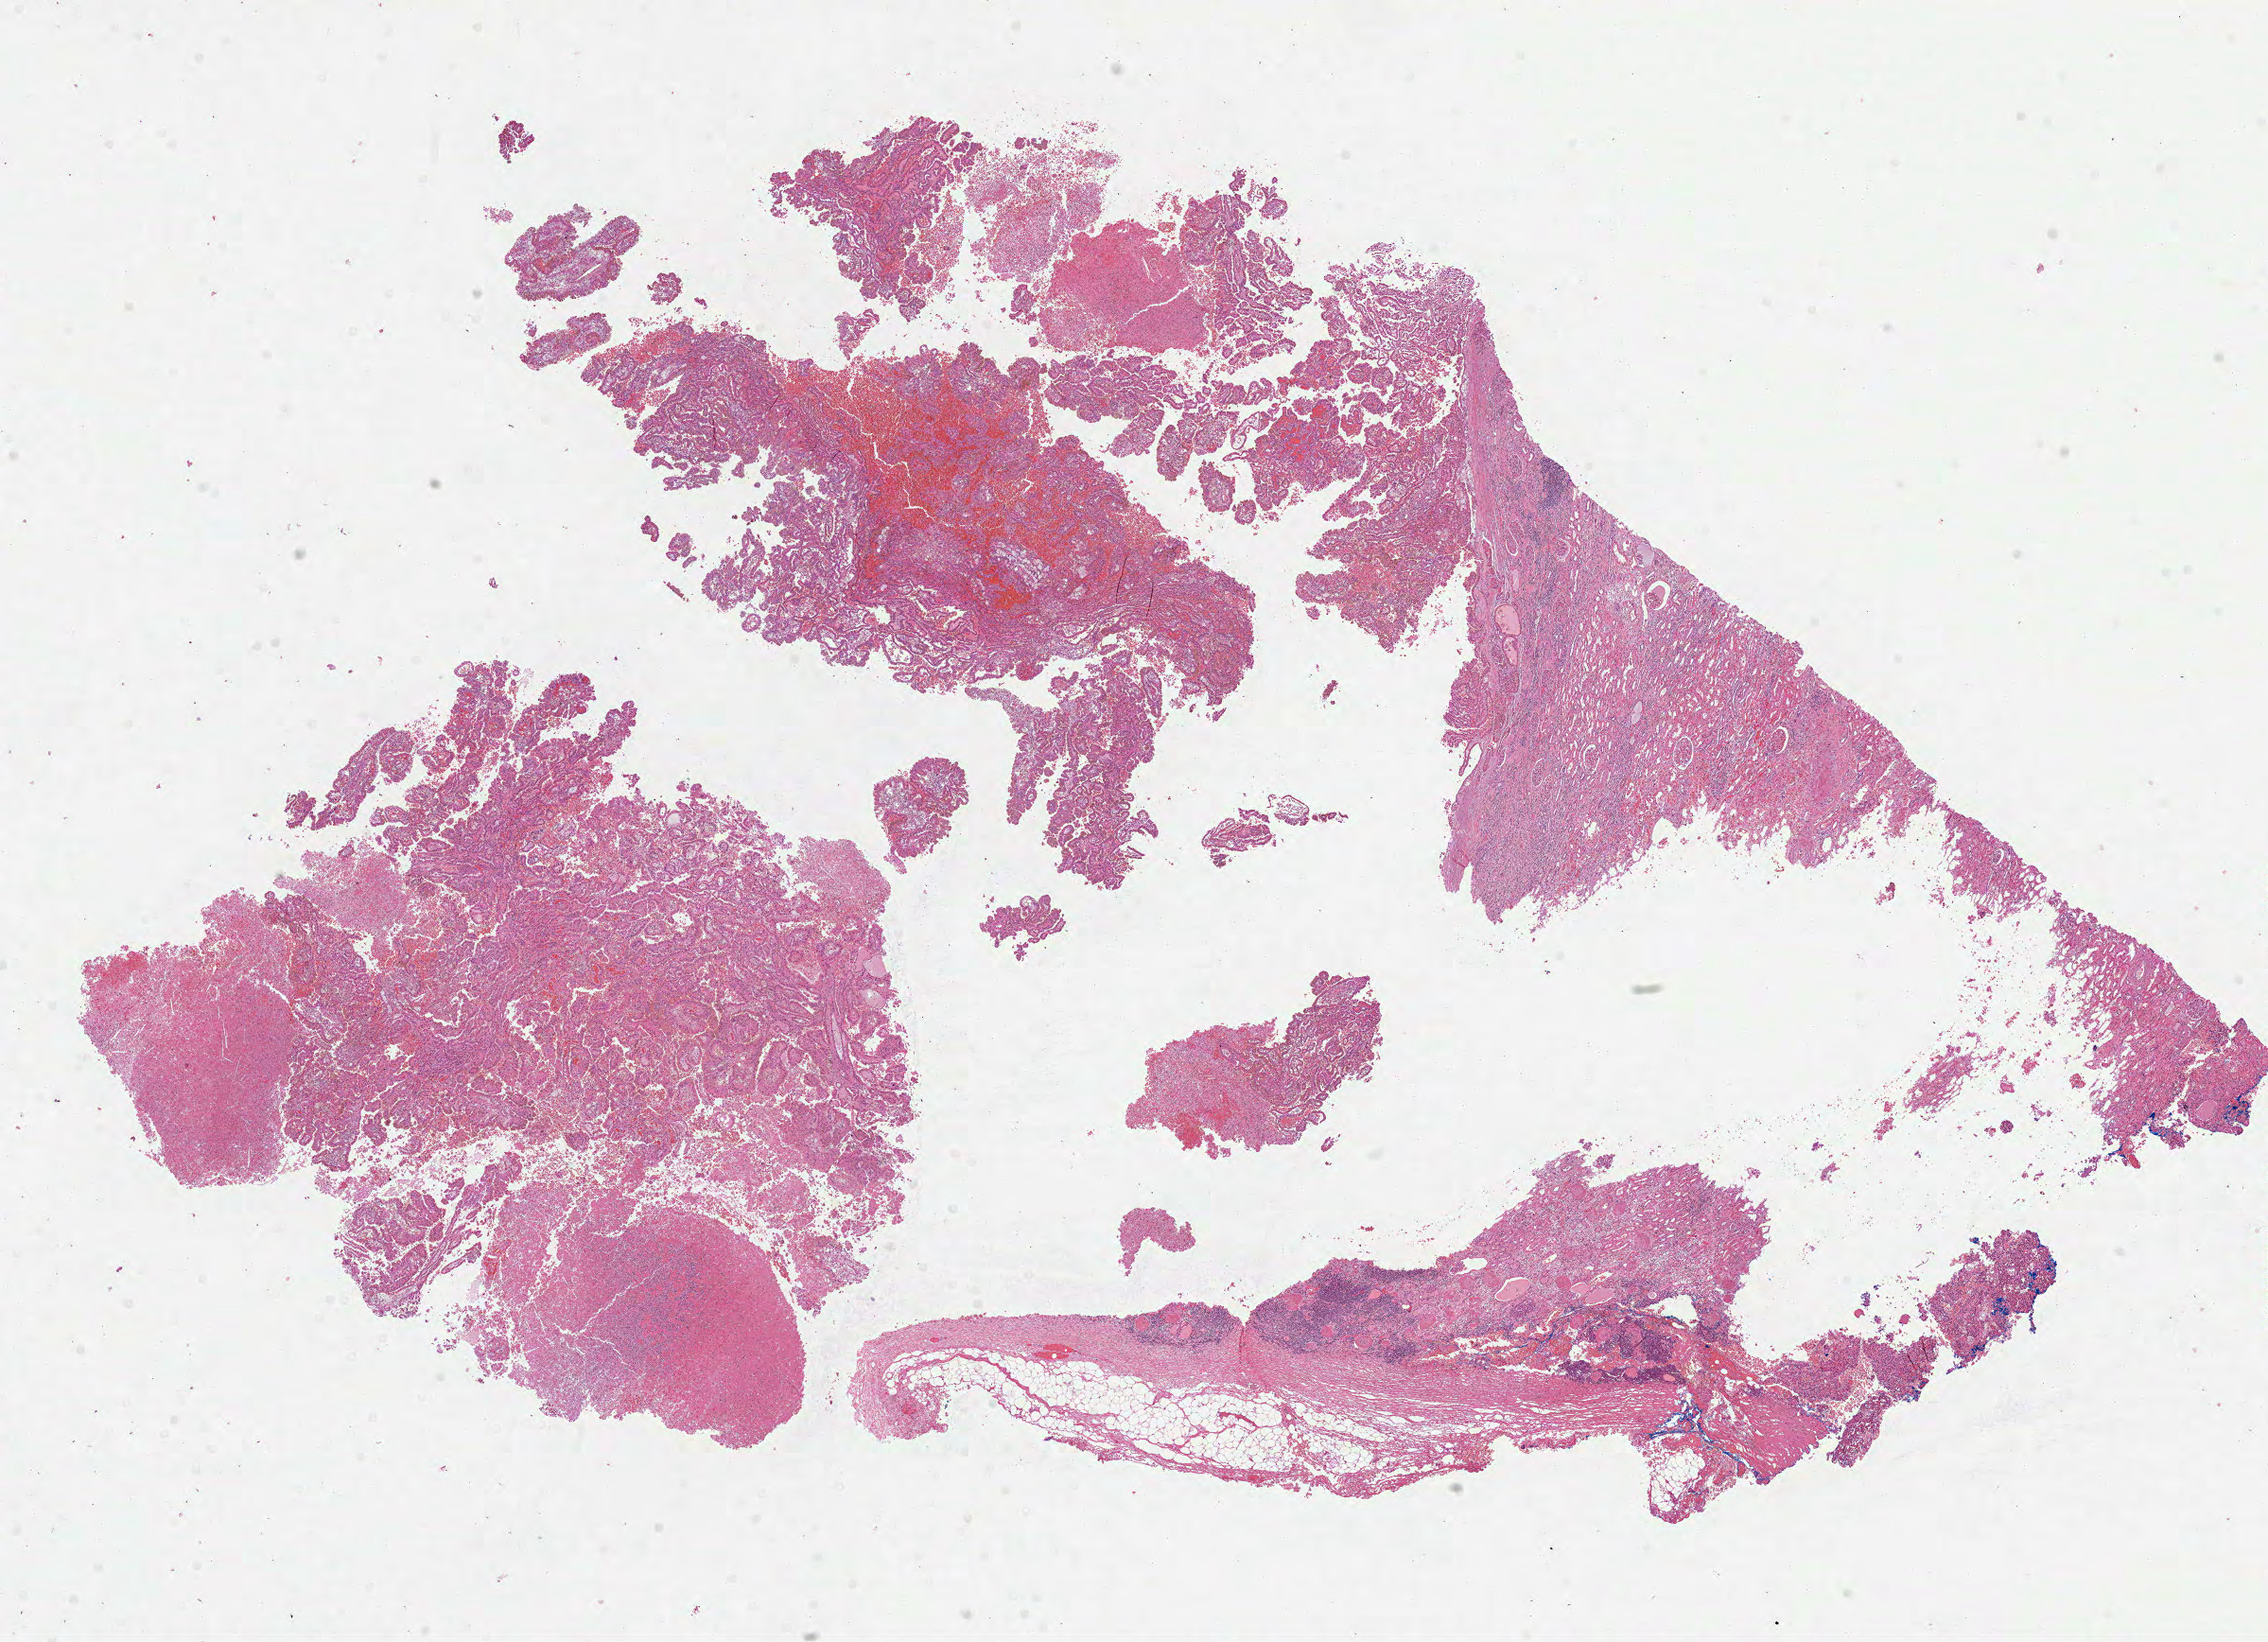
Hematoxylin and eosin (H&E) stained whole-slide image, a low-resolution overview of the entire scanned area, about 19.3 x 14.0 mm; formalin-fixed paraffin-embedded (FFPE) diagnostic section; kidney, primary tumour sample. Male, age 59 years at initial diagnosis.
Diagnosis: Papillary adenocarcinoma, NOS.